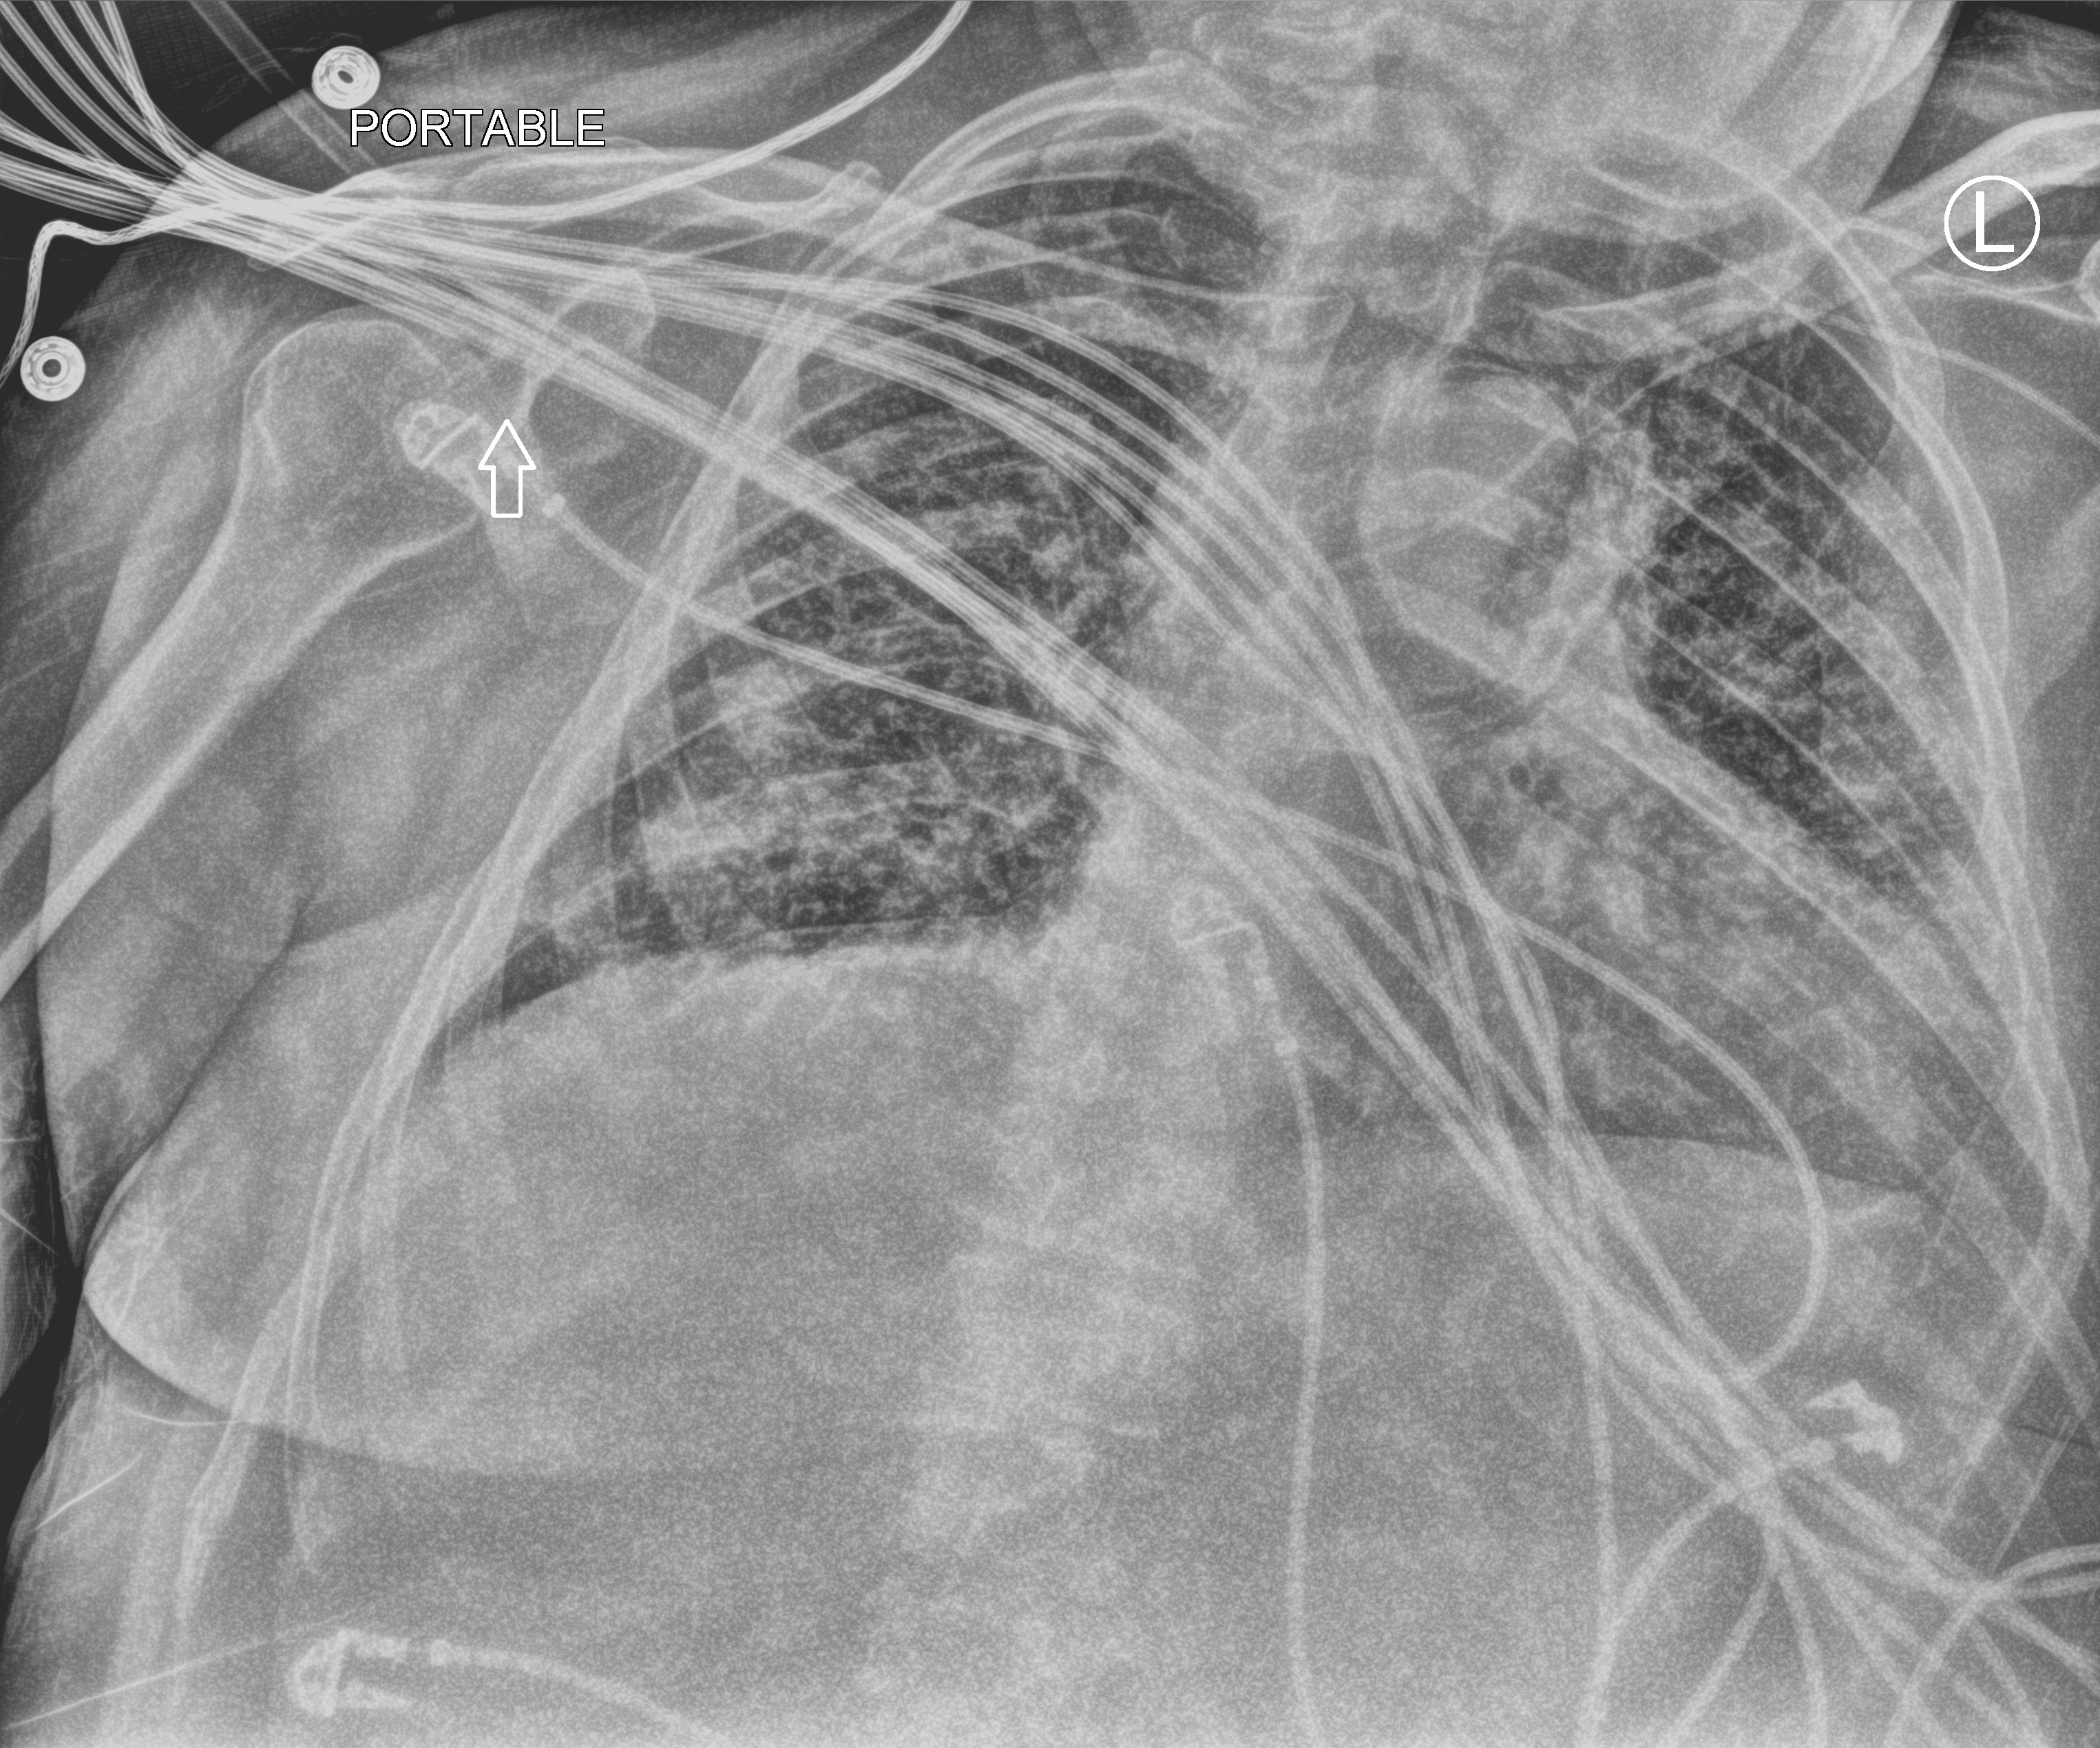
Chest X-ray (portable); anteroposterior (AP) projection. Patient hospitalised with COVID-19; male, aged 18–59 years.
Hospital-stay facts (about this admission, not read from this image; timing relative to this image not recorded): mechanically ventilated during this hospital stay: yes; hypertension (admission record): yes; COPD (admission record): no.